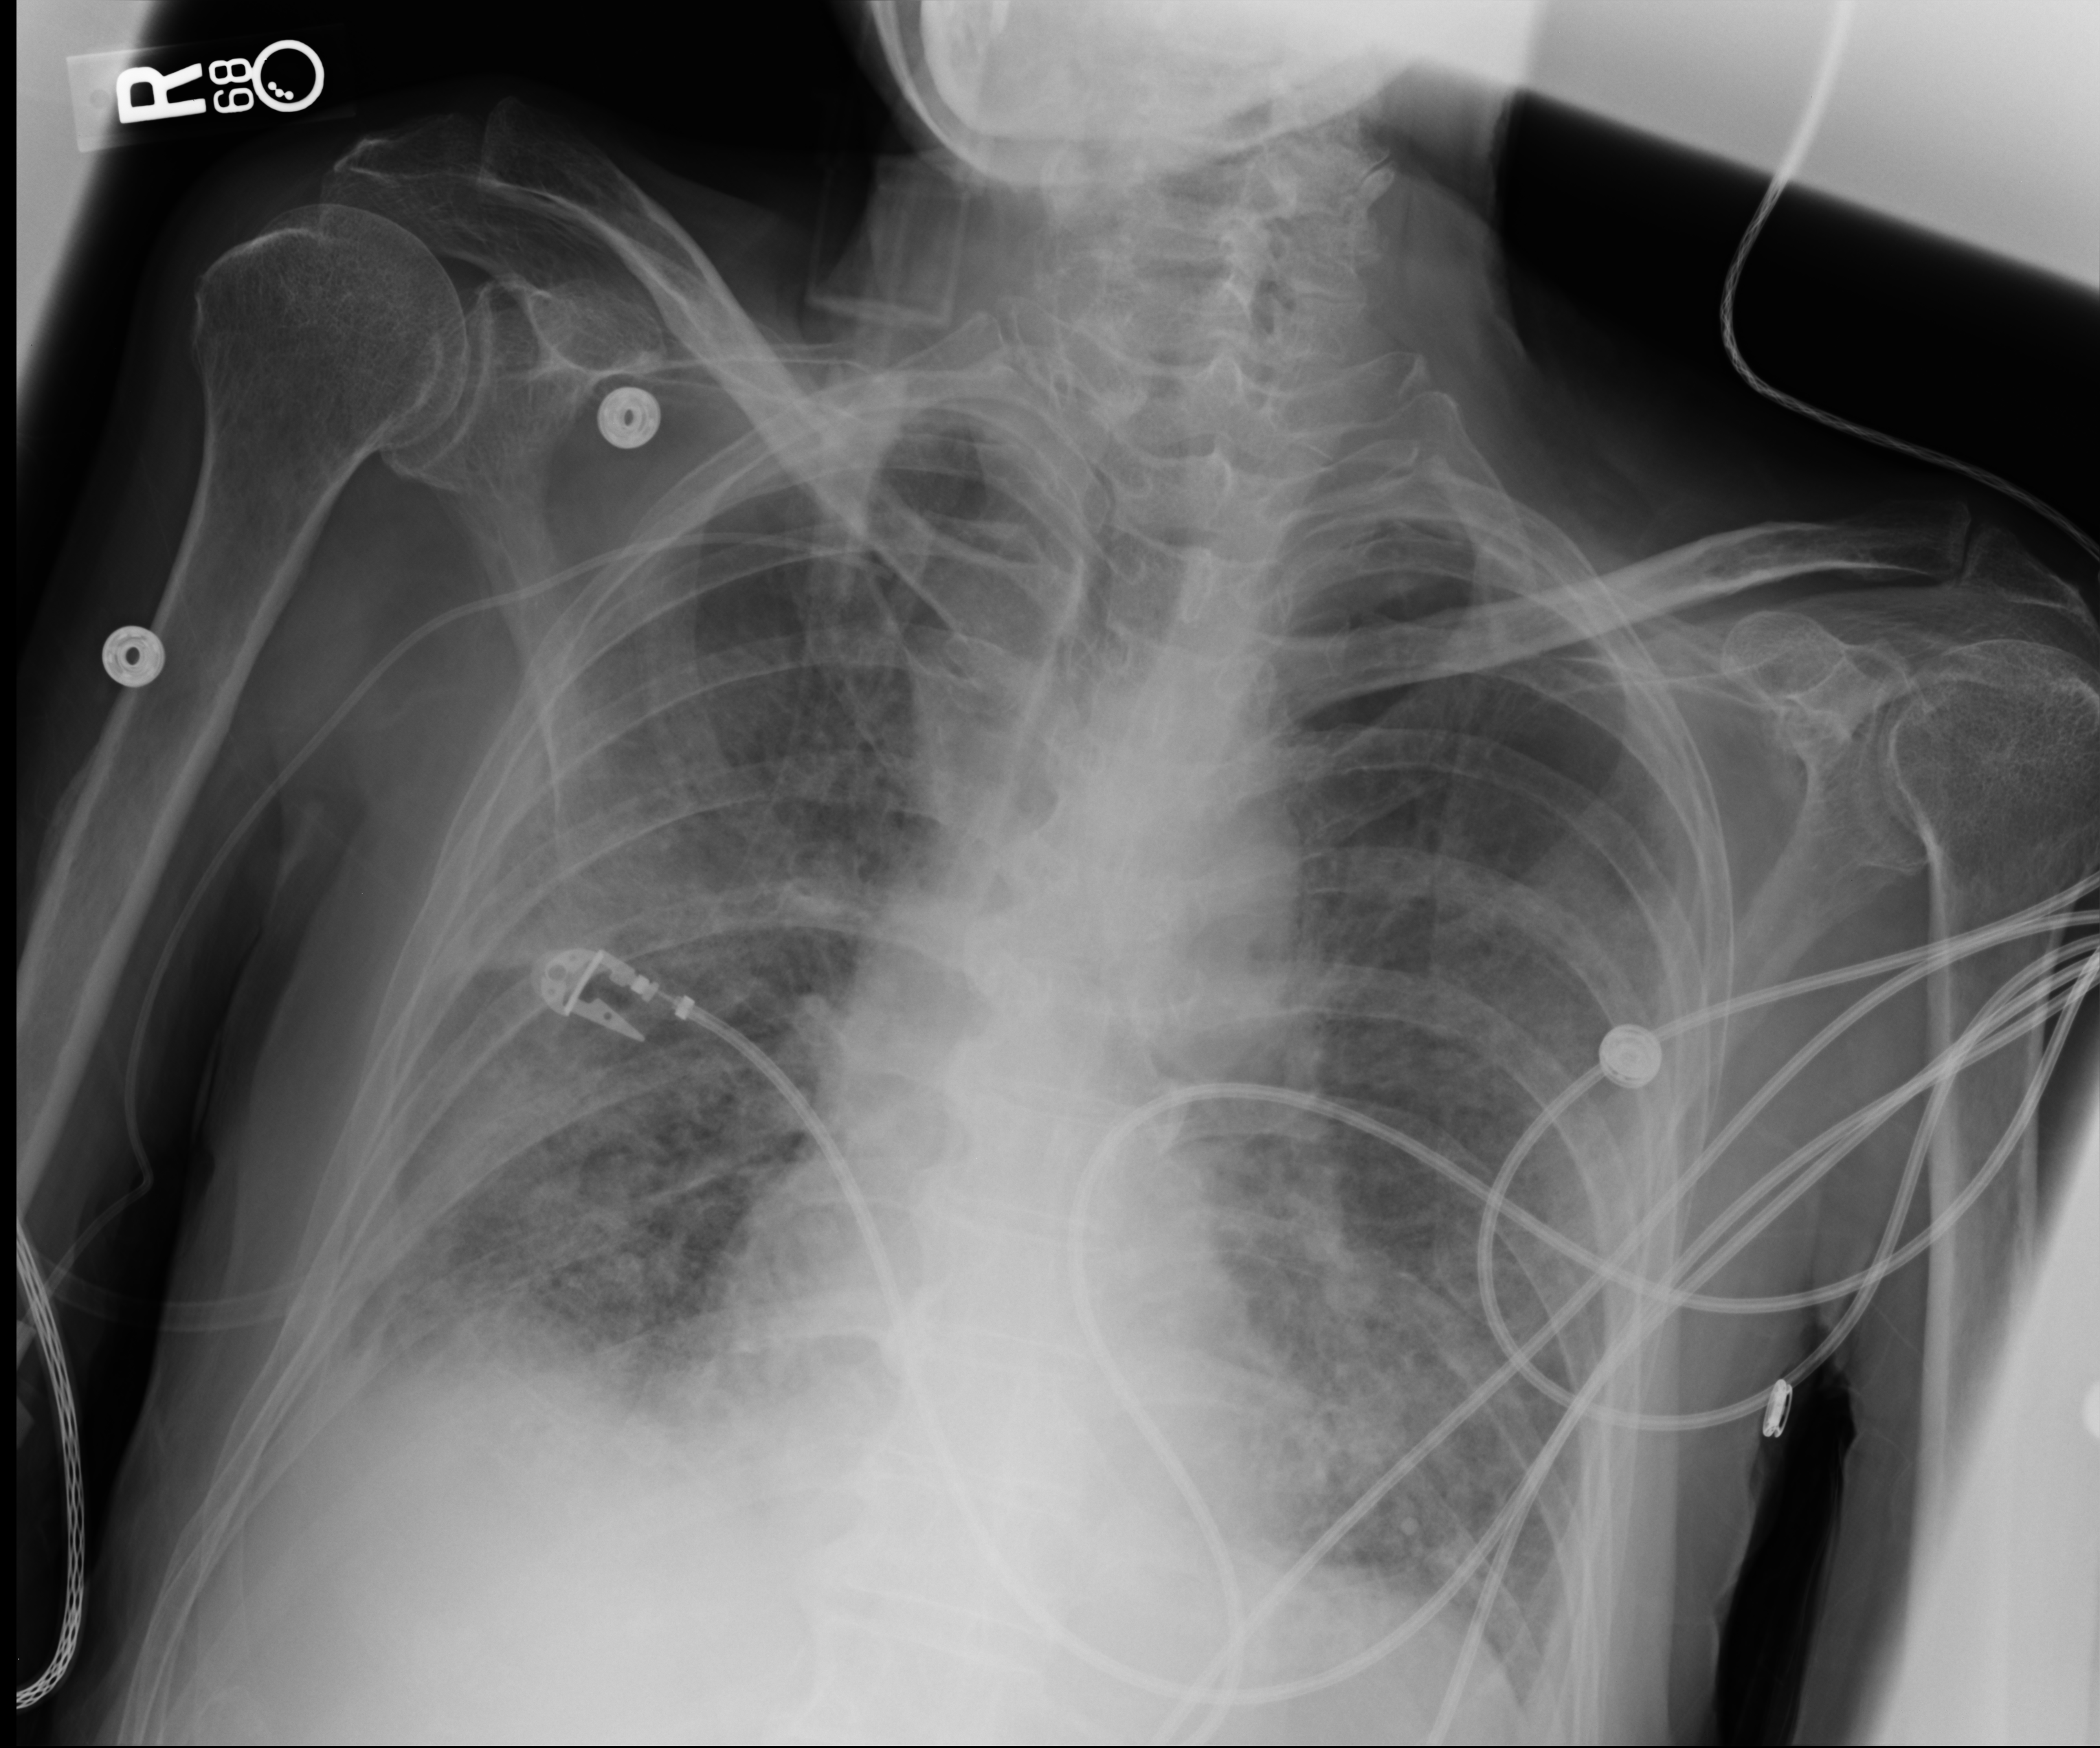
Portable chest radiograph. Male patient hospitalised with COVID-19, age 60–74 years.
Admission-level facts for this patient (not findings on this image; timing relative to this image not recorded): hypertension (admission record): yes; mechanically ventilated during this hospital stay: yes.